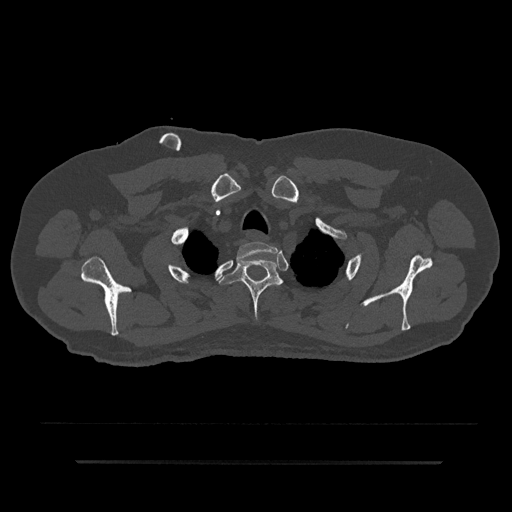
CT including the spine, one axial slice. Position 704 of 797 along the scan axis. Reconstruction kernel Br40s/3. 120 kVp. Bone window (W 1800 / L 400 HU). 0.5 mm slice thickness. 512 × 512 image matrix. Patient: male, 59 years. Case-level facts recorded for this patient, not image findings: primary cancer: bile ducts.
Annotated regions visible in this slice (semi-automatically segmented with operator editing):
- T1 vertebra: bounding box <236,242,278,263> (left, top, right, bottom; pixels)
- T2 vertebra: <219,255,283,321>